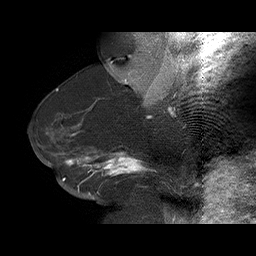
Breast MRI (dynamic contrast-enhanced), one sagittal slice; slice 41 of 75 in the series (ordered by position); dynamic contrast-enhanced series, time point 2 of 6 at this slice position (early post-contrast); 1.5 T; TE 4.5 ms, TR 32.4 ms; 3 mm slice thickness; 256 × 256 image matrix. Female patient. Case-level facts recorded for this patient, not image findings: setting: breast cancer imaged before/during neoadjuvant chemotherapy; receptor status: HR-positive, HER2-negative.
Outlined on this slice (semi-automatically segmented with operator editing):
- analysis volume of interest (the breast-tissue region the enhancement analysis was run in; not a lesion): box from (x=58, y=134) to (x=166, y=191) px
- tumour enhancement mask (voxels above the 100 % enhancement threshold inside the analysis volume of interest): (x=62, y=134)–(x=144, y=183)